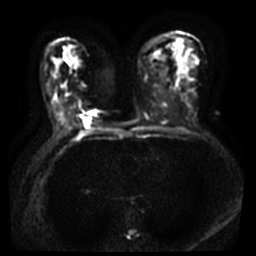
Breast MRI, one axial slice; position 25 of 40 along the scan axis; diffusion-weighted series; image 2 of 4 stored at this slice position (different b-values; order by instance number); 3 T; 5 mm slice thickness; 256 × 256 image matrix, field of view 340 × 340 mm. Female patient.
Structures marked on this image (manually delineated by an expert):
- tumour on diffusion-weighted imaging: bounding box (x1, y1, x2, y2) in pixels: (84, 111, 95, 124)